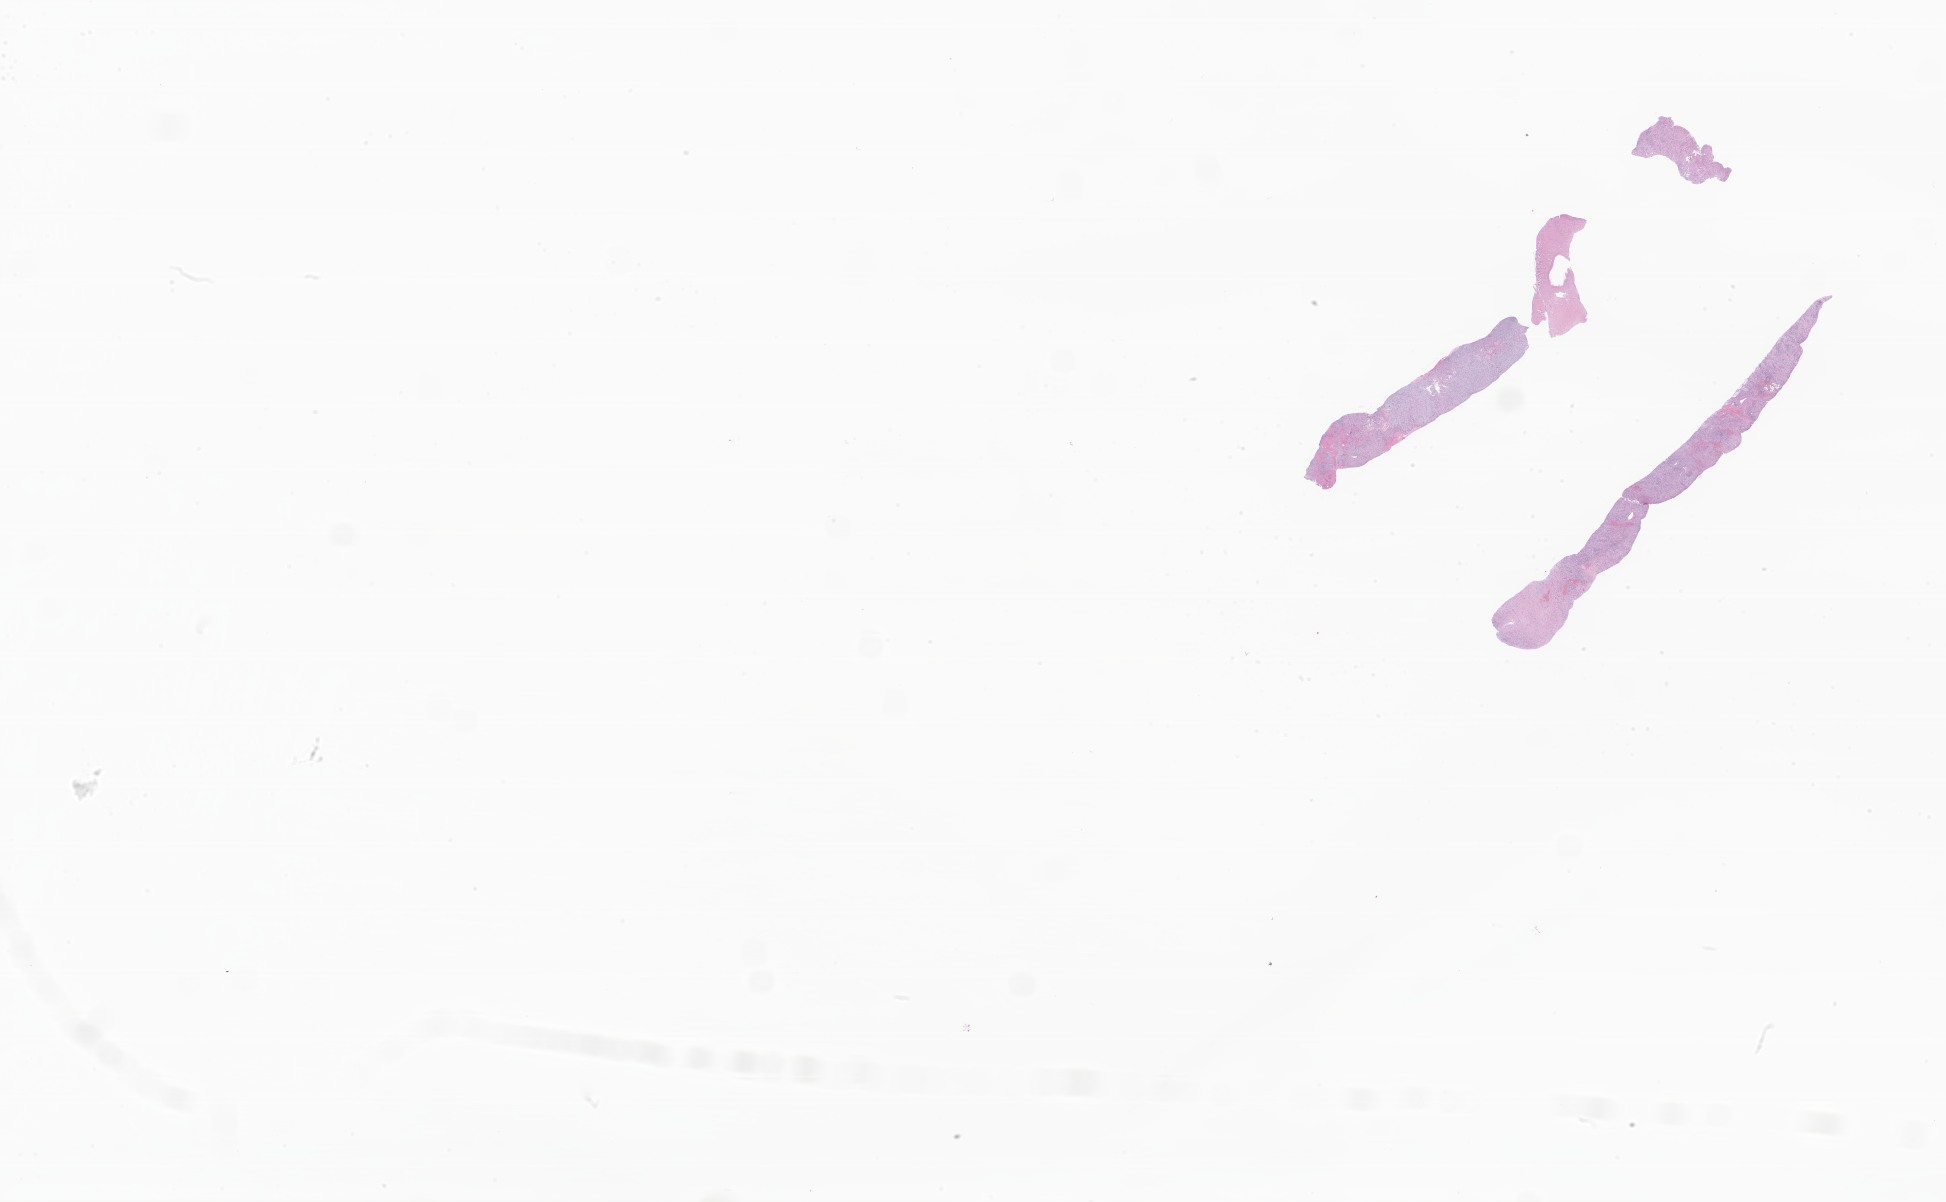
Haematoxylin and eosin whole-slide image of tumor tissue from the soft tissue of thorax — shown as a low-resolution overview of the whole scanned area (about 32.8 x 20.3 mm), FFPE section. Patient male; age 175 months (14 years 7 months).
* diagnosis: Malignant tumor, spindle cell type